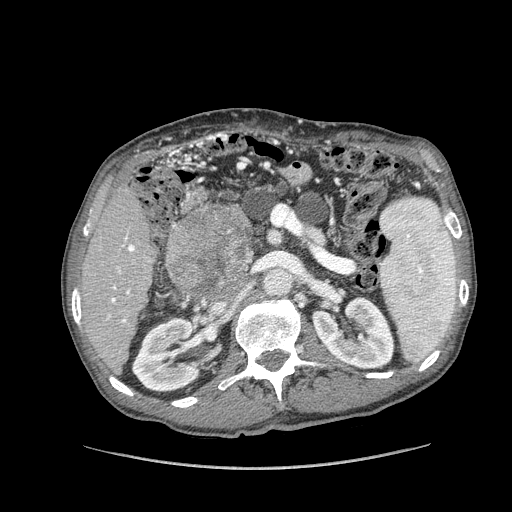
Contrast-enhanced abdominal CT (liver protocol), one axial slice. Slice 53 of 162 in the series (ordered by position). Reconstruction kernel STANDARD. 100 kVp. Soft-tissue window (W 400 / L 40 HU). 2.5 mm slice thickness. 512 × 512 image matrix, field of view 400 × 400 mm. From the clinical record (not read from this slice): diagnosis: hepatocellular carcinoma (patient treated with transarterial chemoembolisation; whether this scan precedes or follows treatment is not stated here); TNM stage (as recorded): Stage-IIIA; Child-Pugh class: A; tumour nodularity: multinodular.
Annotated regions visible in this slice (semi-automatic segmentation, software-assisted and operator-edited):
- liver parenchyma outside the tumour (the mass and vessels are separate outlines, so this box may not span the whole liver): bounding box <80,184,156,370> (left, top, right, bottom; pixels)
- mass: <166,205,253,294>
- liver vessels: <107,236,135,323>